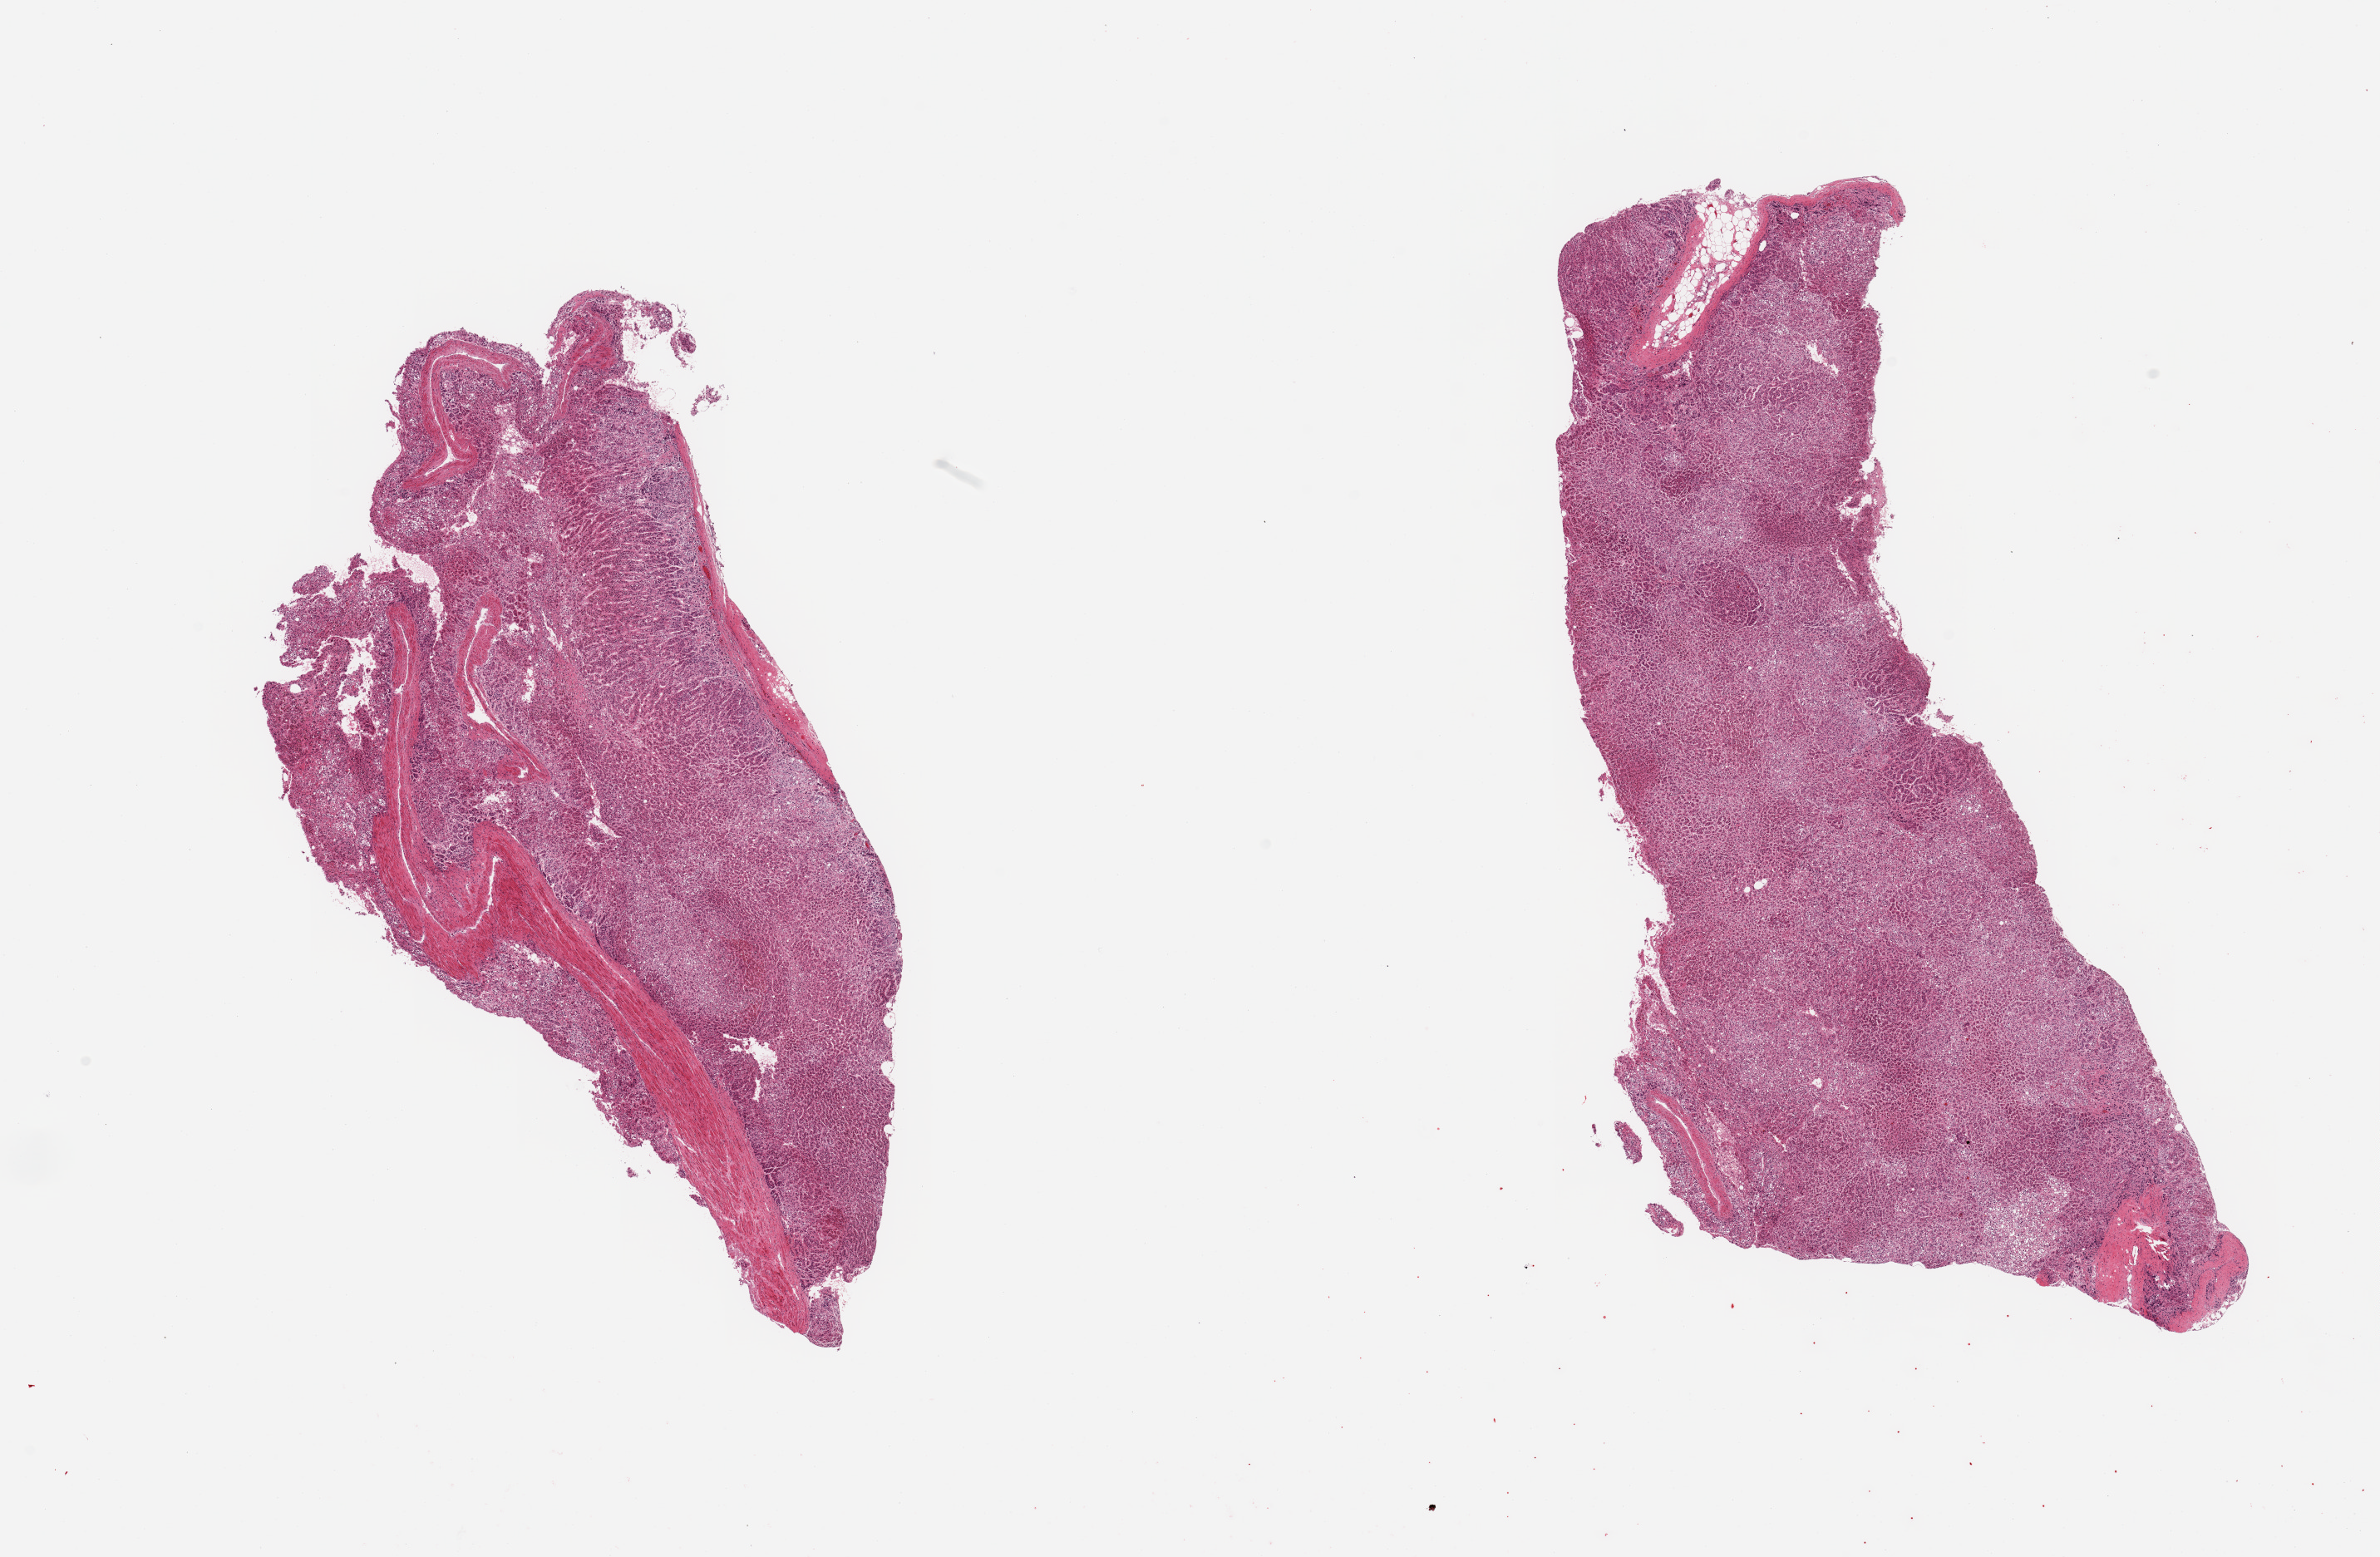
Whole-slide image, hematoxylin and eosin (H&E) stain — shown as a low-resolution overview of the whole scanned area (about 22.6 x 14.8 mm). PAXgene-fixed paraffin-embedded (PFPE) section. Target tissue: adrenal gland. Tissue donor sample. Donor sex: male.
- review note (as recorded): 2 pieces; autolyzed cortex with prominent vessels